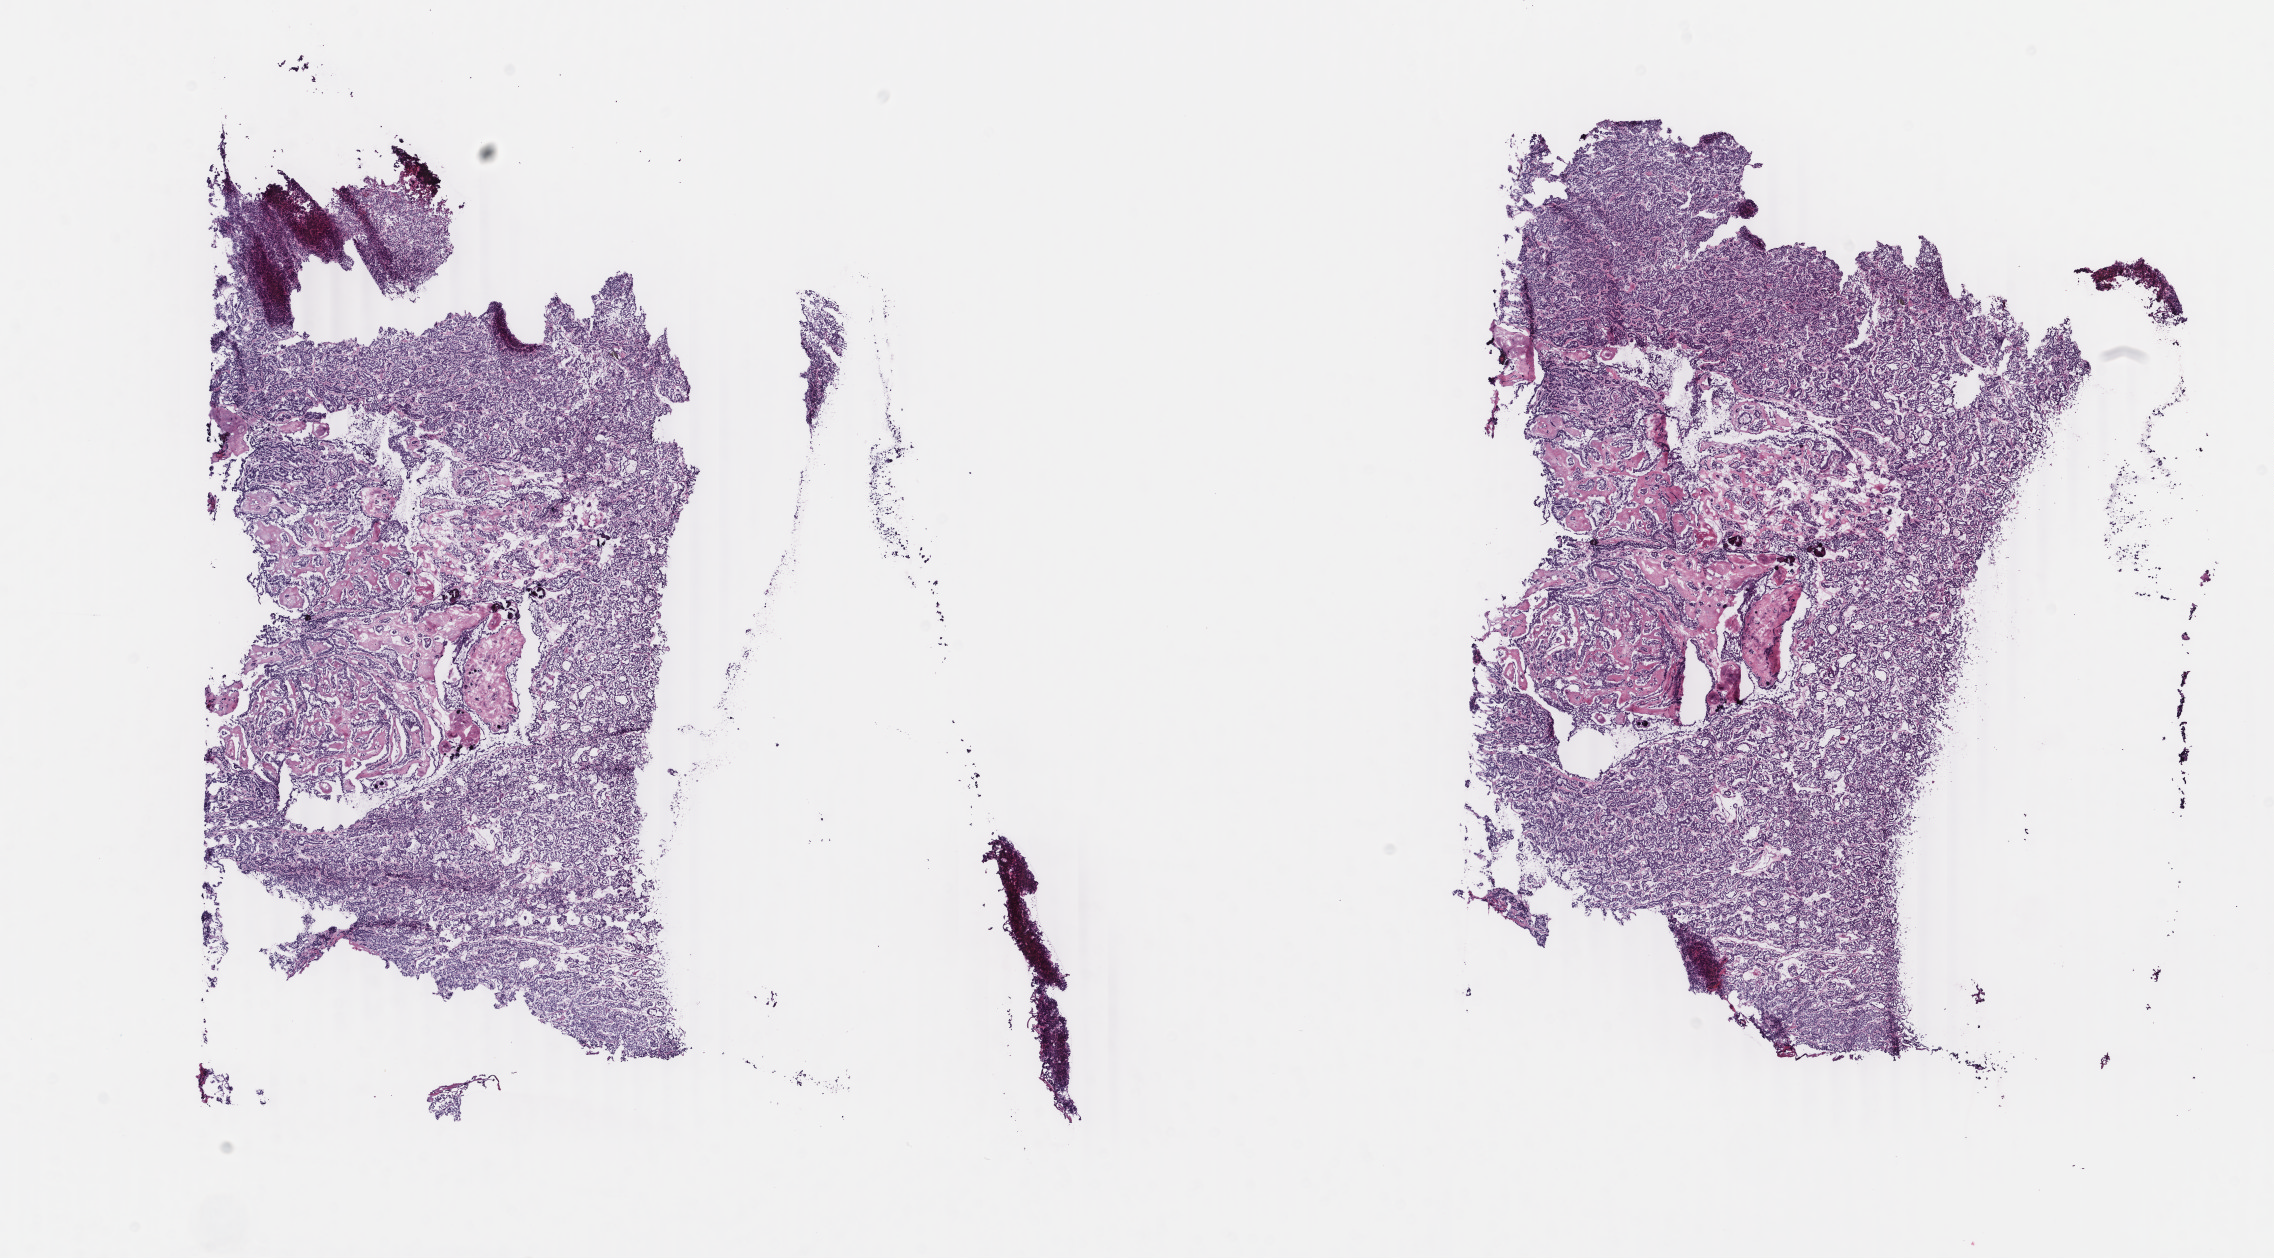
Whole-slide histology image, Hematoxylin and eosin (H&E) stained, whole scanned area (about 18.1 x 10.0 mm) shown as a low-resolution overview. Frozen section from the top of the tissue portion. Thyroid, primary tumour sample. Female, age 52 years at initial diagnosis. Composition of this section per pathologist review: tumour cells 100%, tumour nuclei 95%, normal cells 0%, stromal cells 0%, necrosis 0%. Inflammatory infiltration, as recorded: lymphocyte infiltration 0%, monocyte infiltration 0%, neutrophil infiltration 0%.
• TNM: T2 N0 M0
• AJCC pathologic stage: II
• pathologic diagnosis: Papillary adenocarcinoma, NOS (thyroid gland)